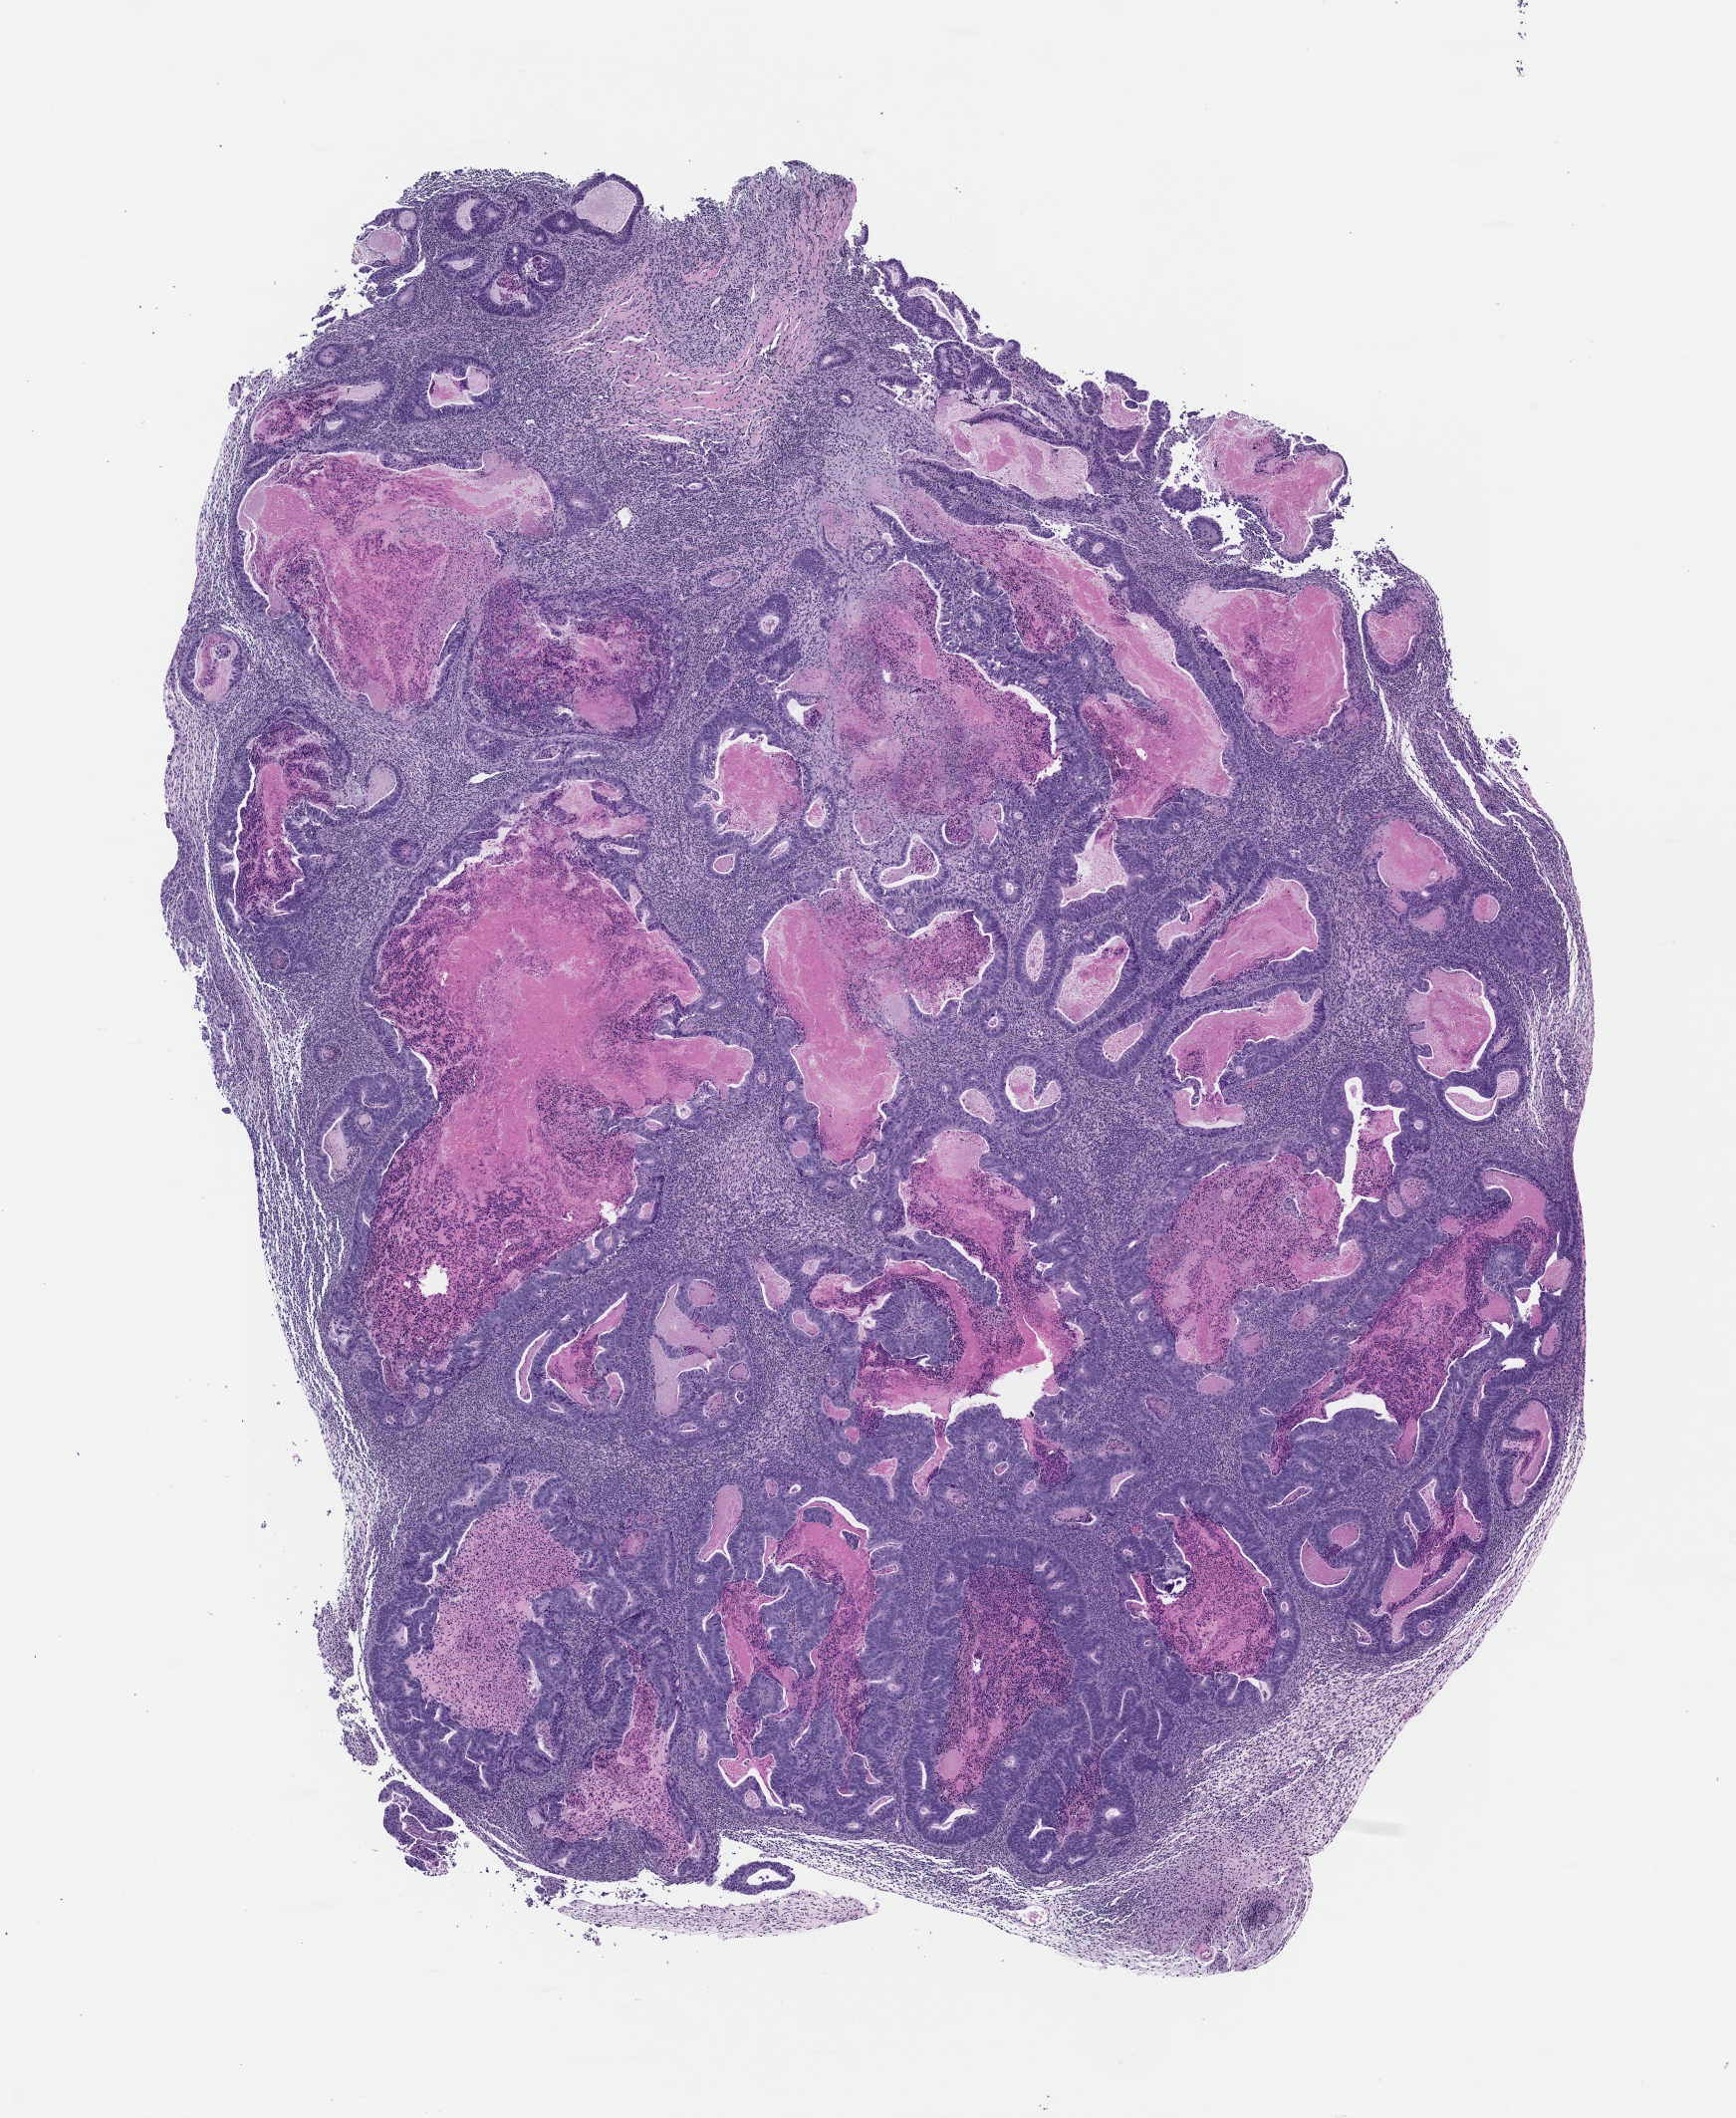
Haematoxylin and eosin whole-slide image of a patient-derived xenograft (PDX) tumor grown in a mouse, passage 0 — a low-resolution overview of the entire scanned area, about 7.0 x 8.5 mm; FFPE section; originating tumor site category: colon.
- originating patient diagnosis: Colon Adenocarcinoma